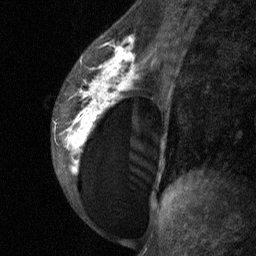
Breast MRI (dynamic contrast-enhanced), one sagittal slice. Position 40 of 64 along the scan axis. Dynamic contrast-enhanced study with each time point stored as its own series, time point 2 of 3 at this slice position (early post-contrast, ordered by acquisition time). 1.5 T. TE 4.8 ms, TR 27 ms. 2 mm slice thickness. 256 × 256 image matrix, field of view 180 × 180 mm. Patient: female, 34 years. Case-level facts recorded for this patient, not image findings: setting: breast cancer imaged before/during neoadjuvant chemotherapy; receptor status: HR-positive, HER2-negative.
Structures marked on this image (semi-automatic segmentation, software-assisted and operator-edited):
- analysis volume of interest (the breast-tissue region the enhancement analysis was run in; not a lesion): box from (x=51, y=23) to (x=157, y=197) px
- tumour enhancement mask (voxels above the 90 % enhancement threshold inside the analysis volume of interest): (x=64, y=35)–(x=137, y=173)